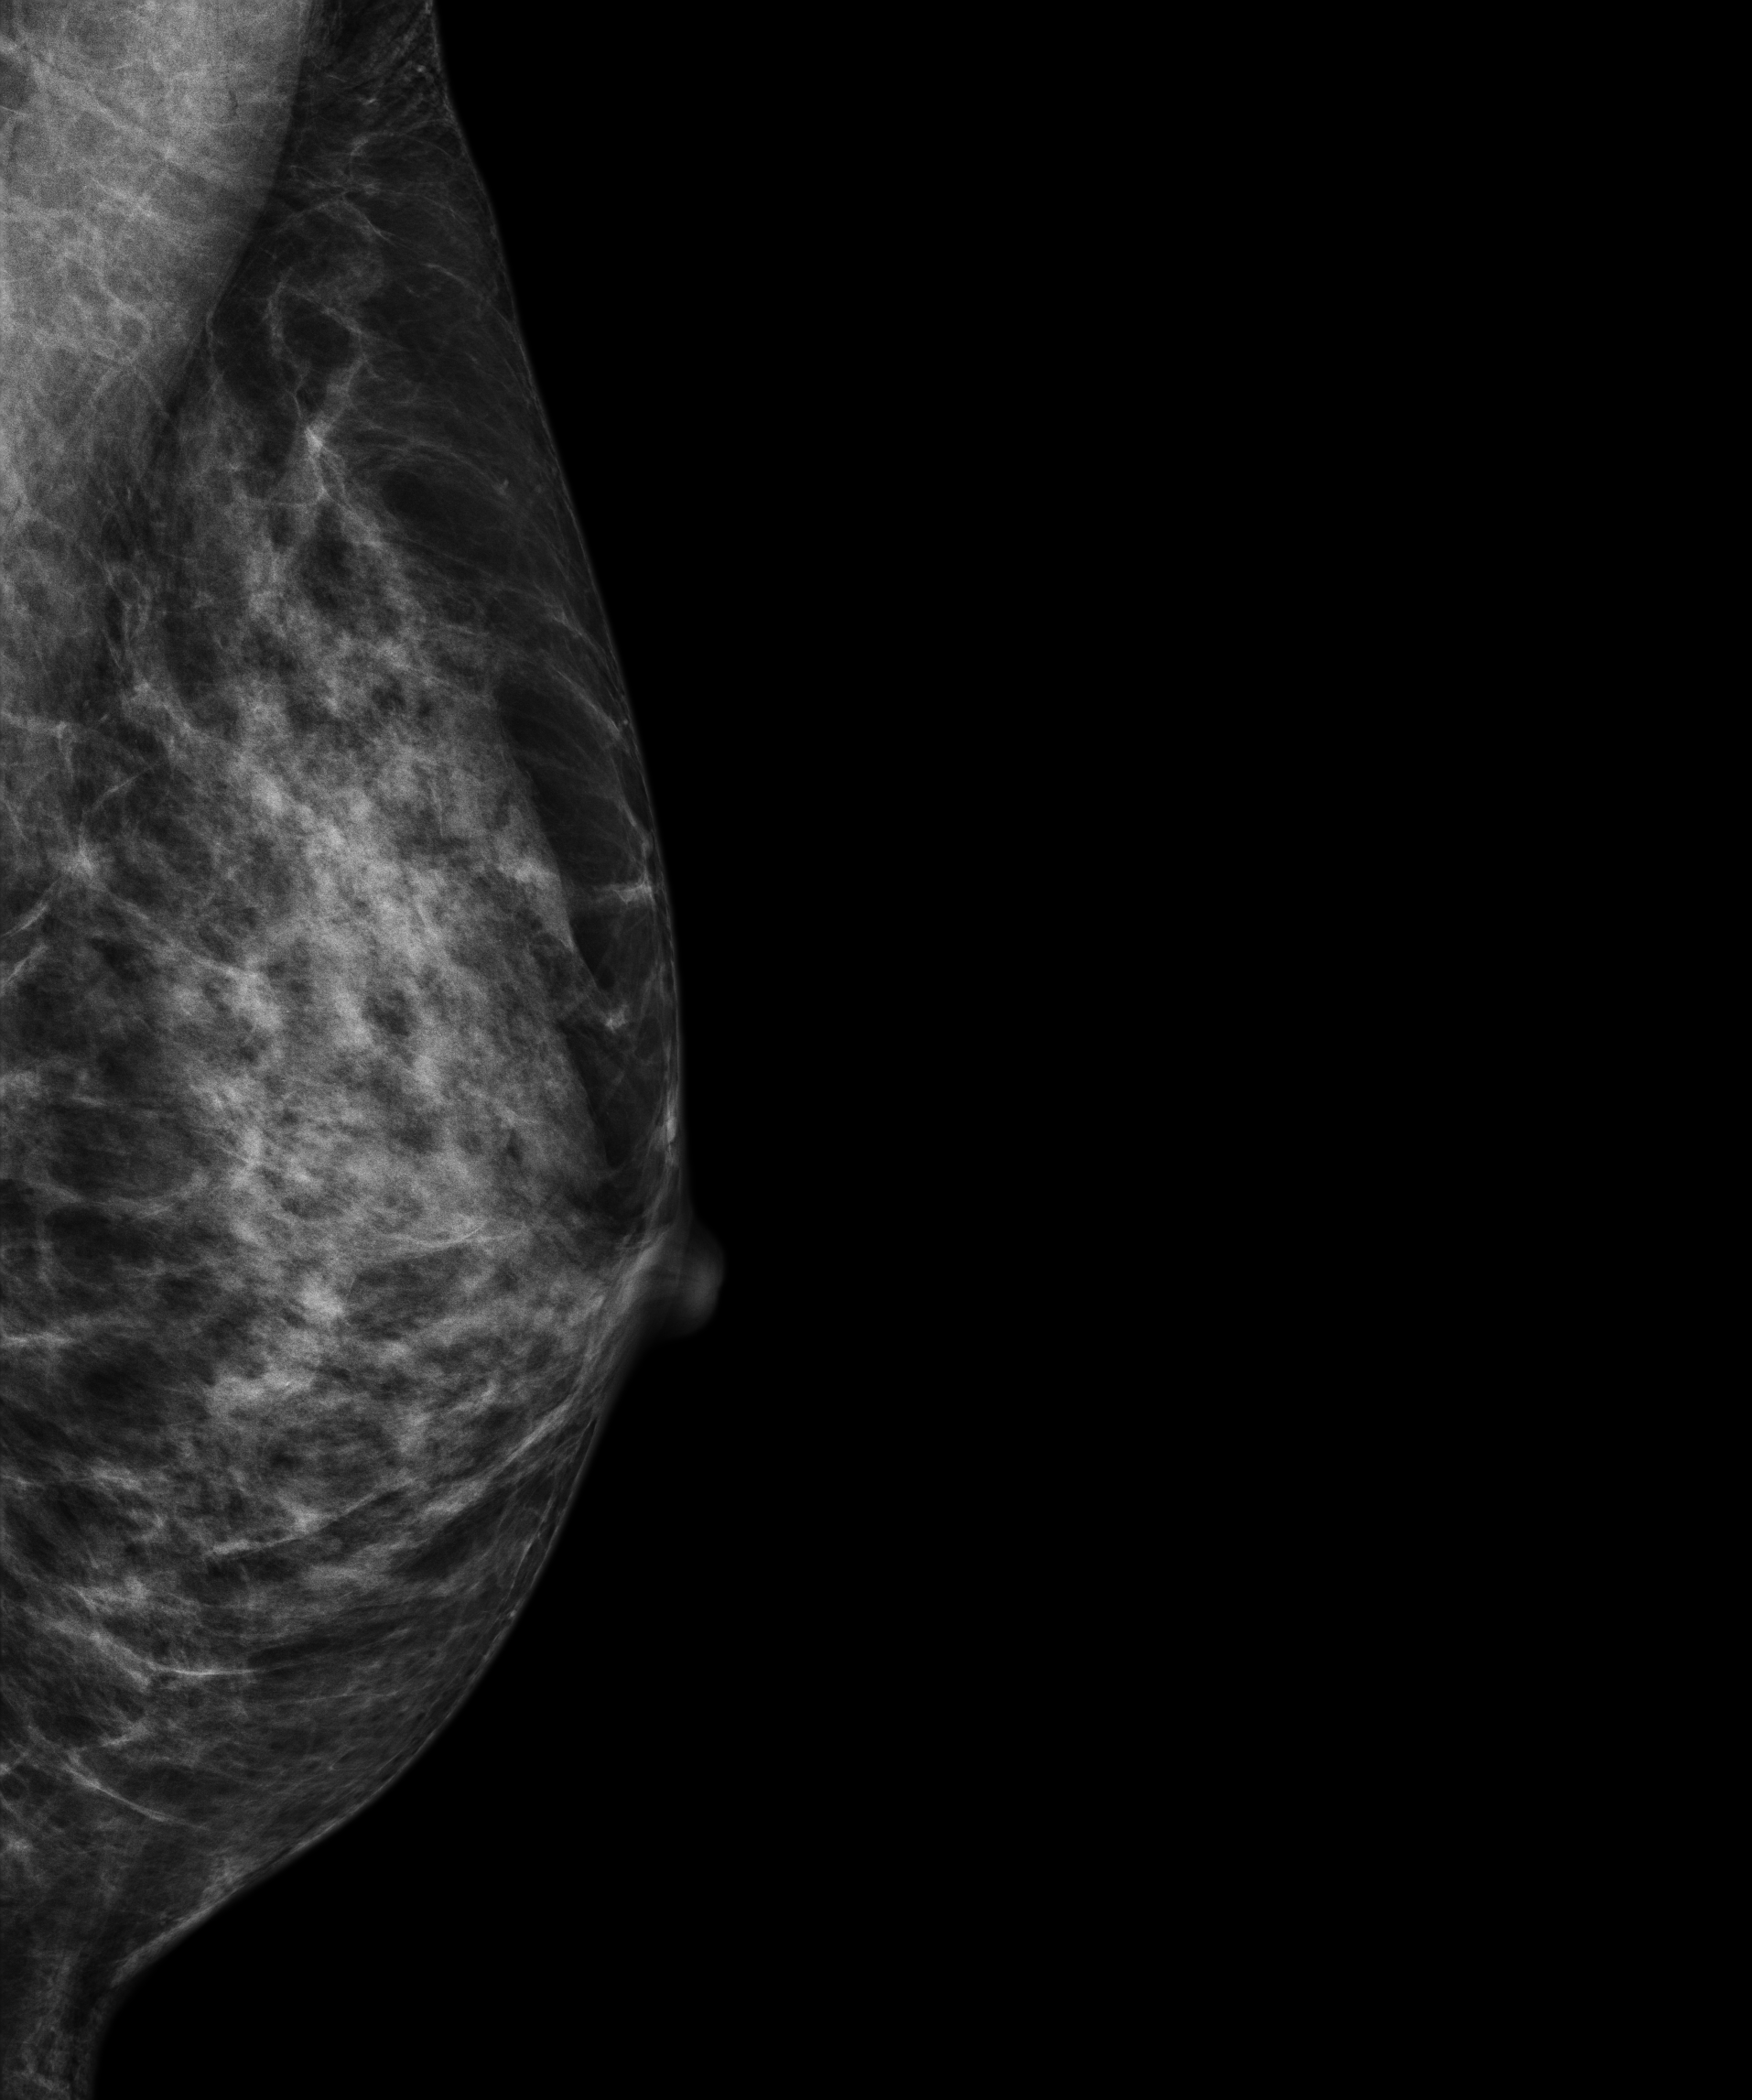
Digital mammogram (FFDM), left breast, medio-lateral oblique projection, screening examination. Patient aged 56 years (female).
Breast density at the screening exam (both breasts): heterogeneously dense (BI-RADS density category c). Final BI-RADS category for the screening round (tomosynthesis exam, both breasts): category 1. Recall: no recall after this screen.